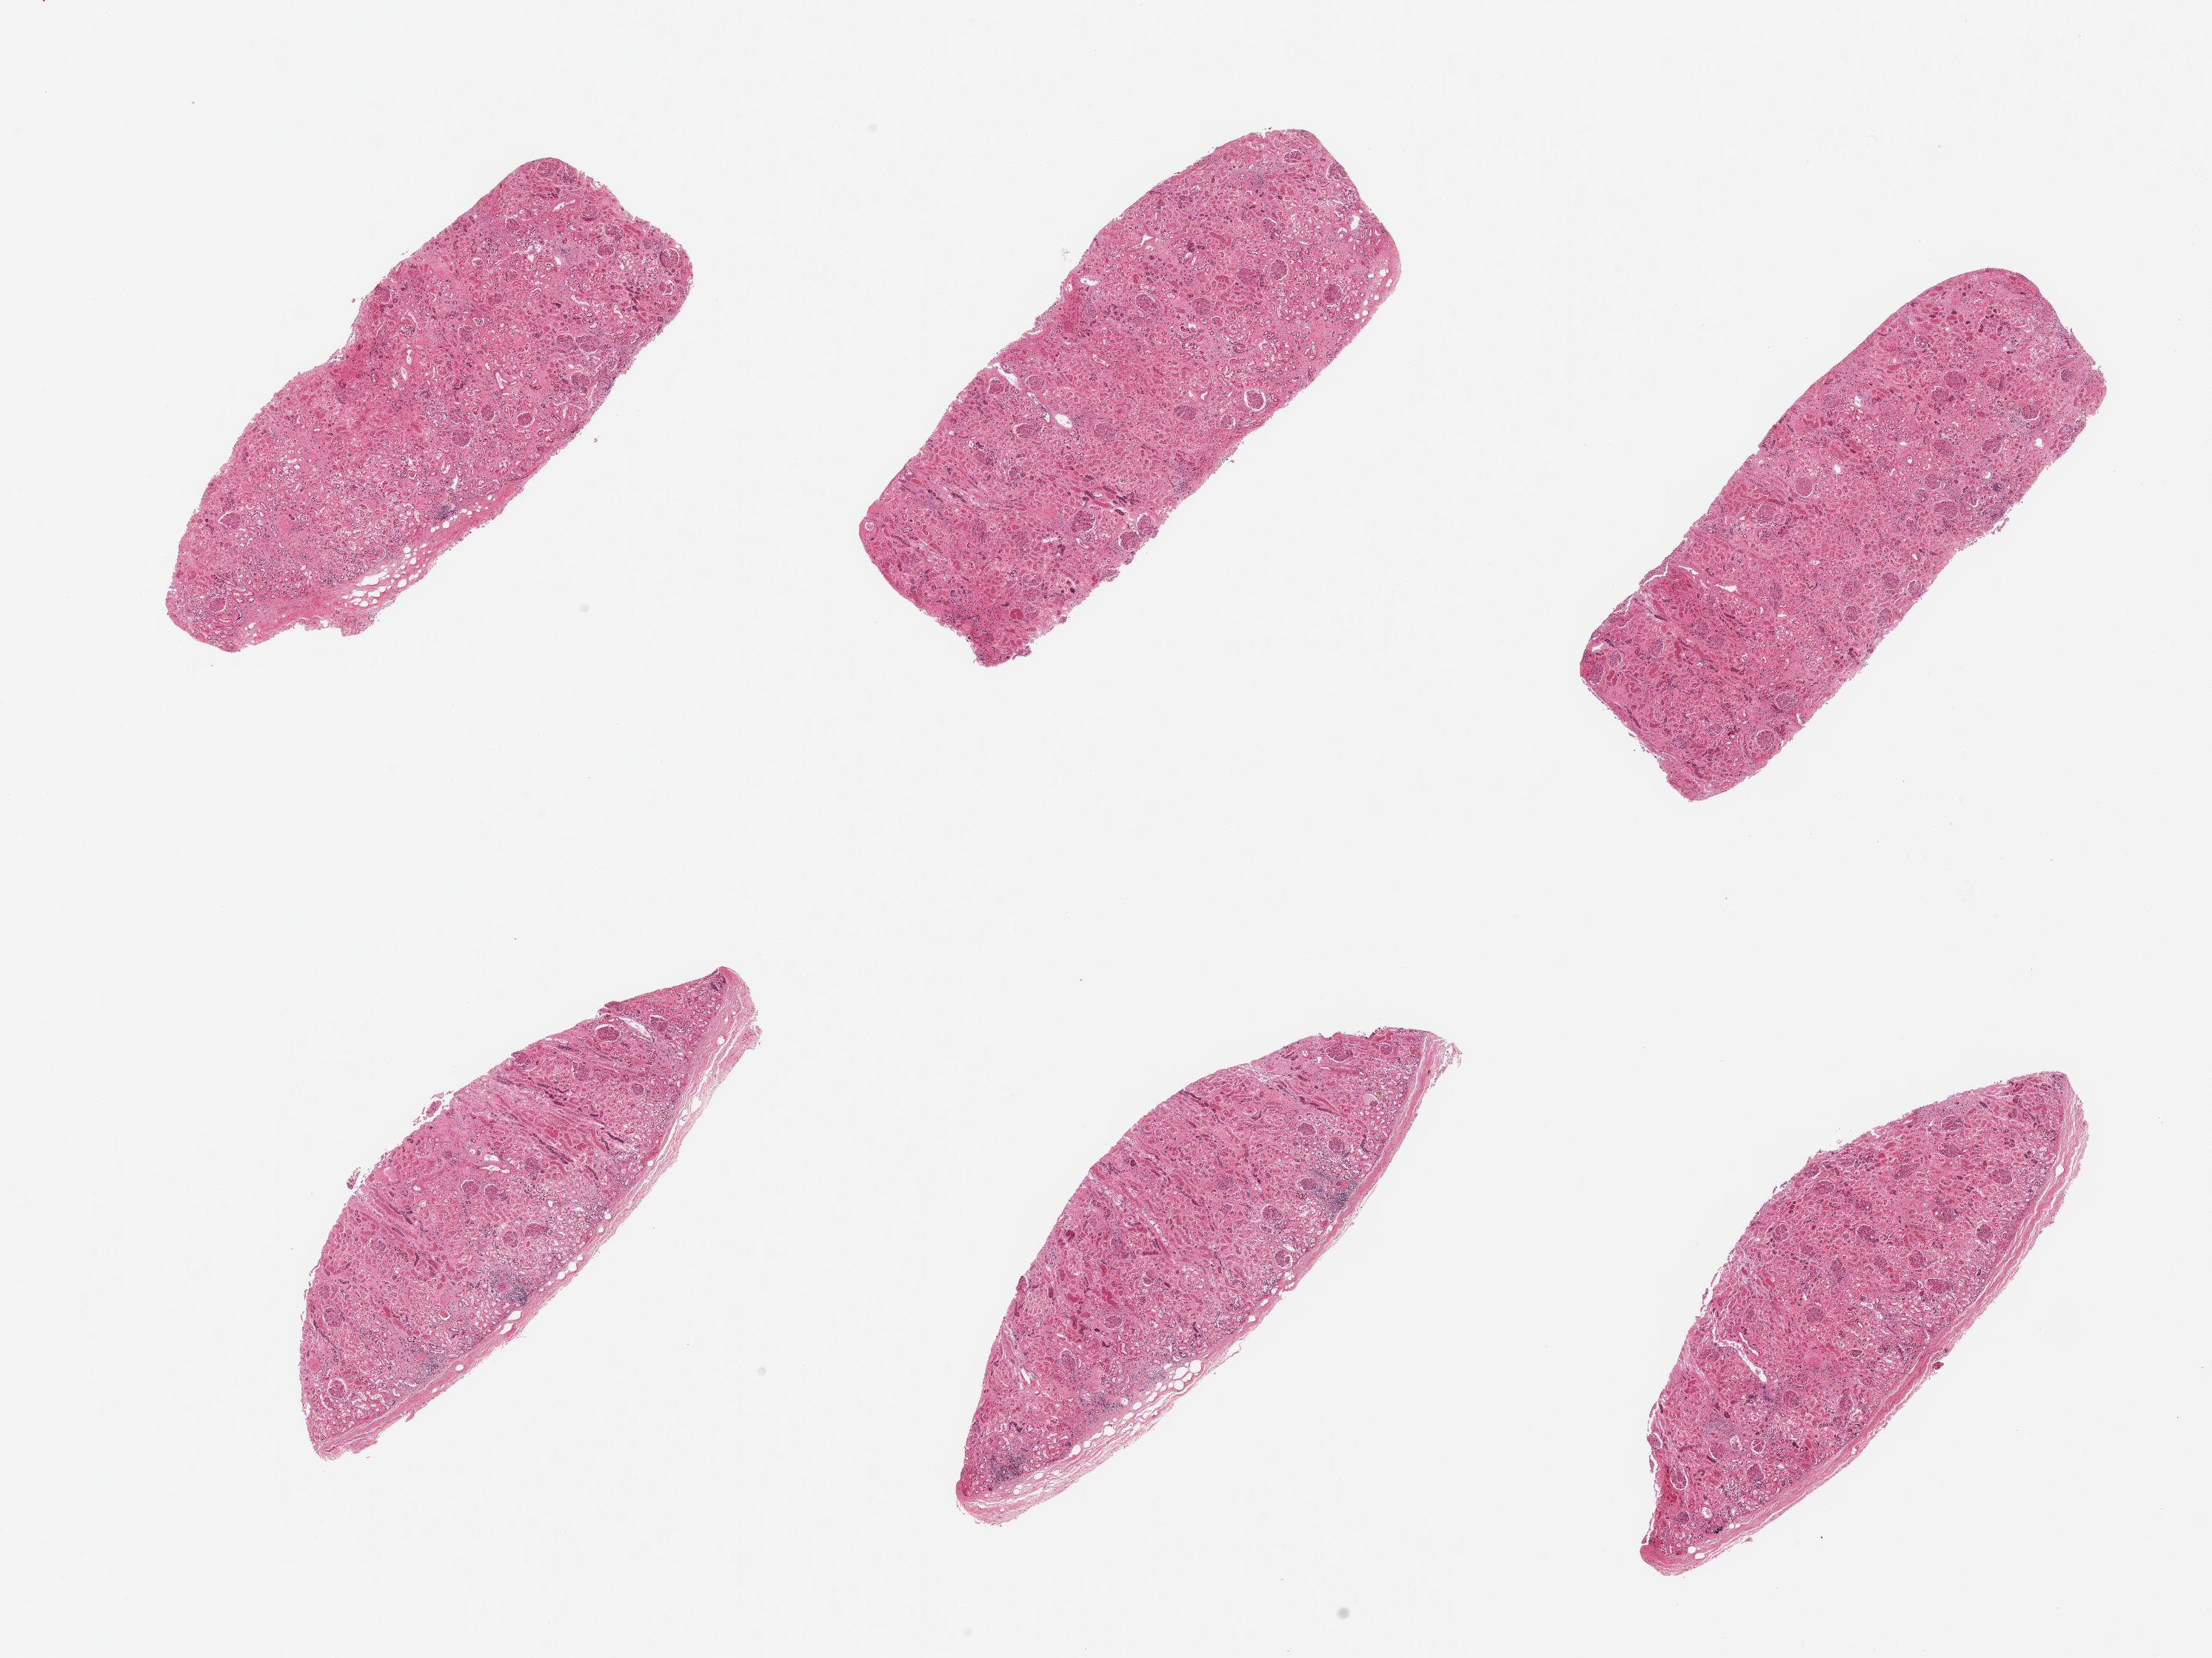
Digitized hematoxylin and eosin (H&E)-stained section, low-resolution overview of the scanned area, about 23.6 x 17.7 mm; PAXgene-fixed paraffin-embedded (PFPE) section; target tissue: renal cortex; donor tissue sample.
* review note (as recorded): 6 pieces, glomeruli present, tubular cells with advanced autolysis